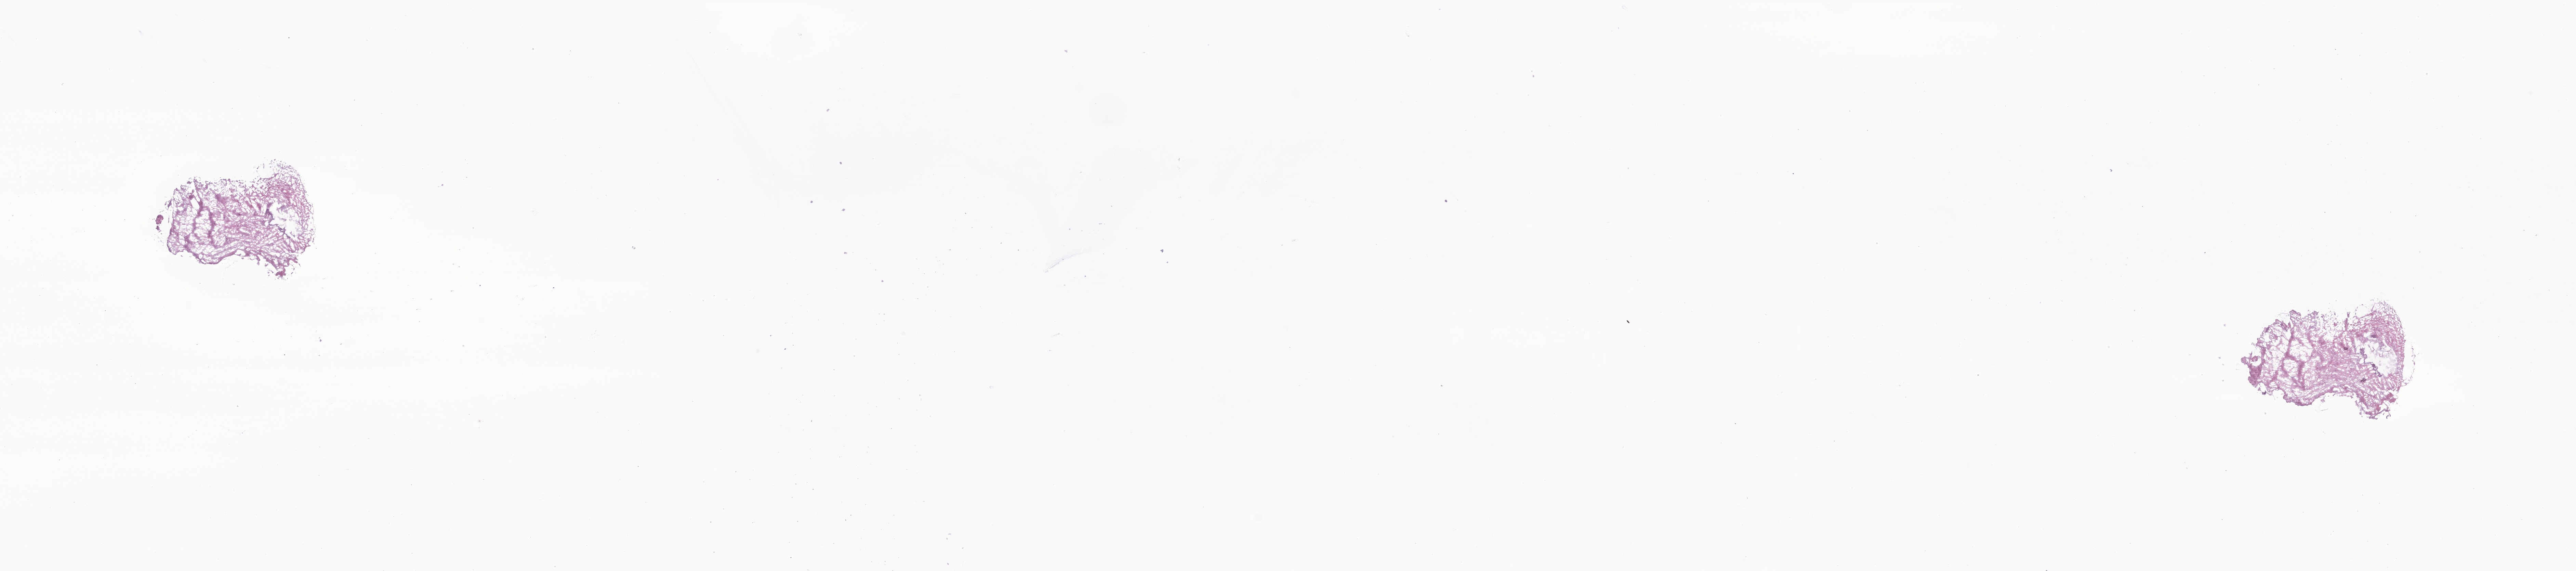
Hematoxylin and eosin (H&E) whole-slide image of tumor tissue from the brain, low-resolution overview of the scanned area, about 31.8 x 7.0 mm, frozen section (OCT-embedded). Male patient, age 91 months (7 years 7 months).
• diagnosis (ICD-O-3 morphology term): Craniopharyngioma, adamantinomatous